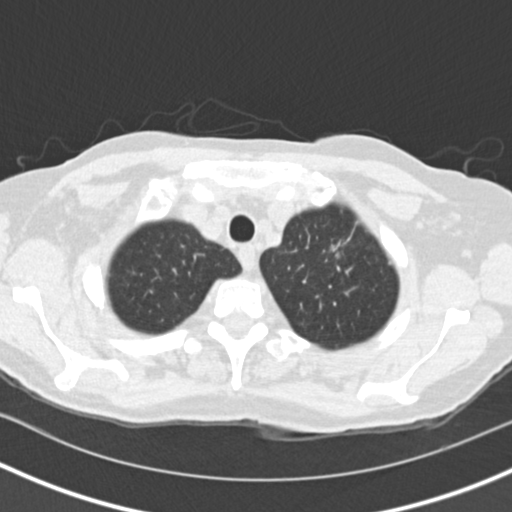
Low-dose screening chest CT, one axial slice. Slice 126 of 146 in the series (ordered by position). Lung window (W 1500 / L -600 HU). 2 mm slice thickness. 512 × 512 image matrix, field of view 310 × 310 mm.
Annotated regions visible in this slice (manually delineated by an expert):
- lesion 1 (tumor, upper lobe of left lung): bounding box (x1, y1, x2, y2) in pixels: (331, 245, 339, 251)